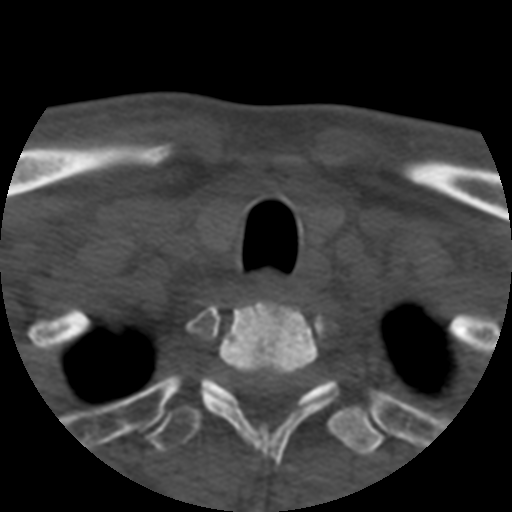
CT including the spine, one axial slice; position 442 of 508 along the scan axis; reconstruction kernel STANDARD; bone window (W 1800 / L 400 HU); 1.25 mm slice thickness; 512 × 512 image matrix, field of view 160 × 160 mm. Patient age 57 years. Case-level facts recorded for this patient, not image findings: primary cancer: prostate.
Annotated regions visible in this slice (semi-automatic segmentation, software-assisted and operator-edited):
- T1 vertebra: bounding box [x1, y1, x2, y2] px = [166, 300, 339, 460]
- T2 vertebra: [146, 376, 385, 456]